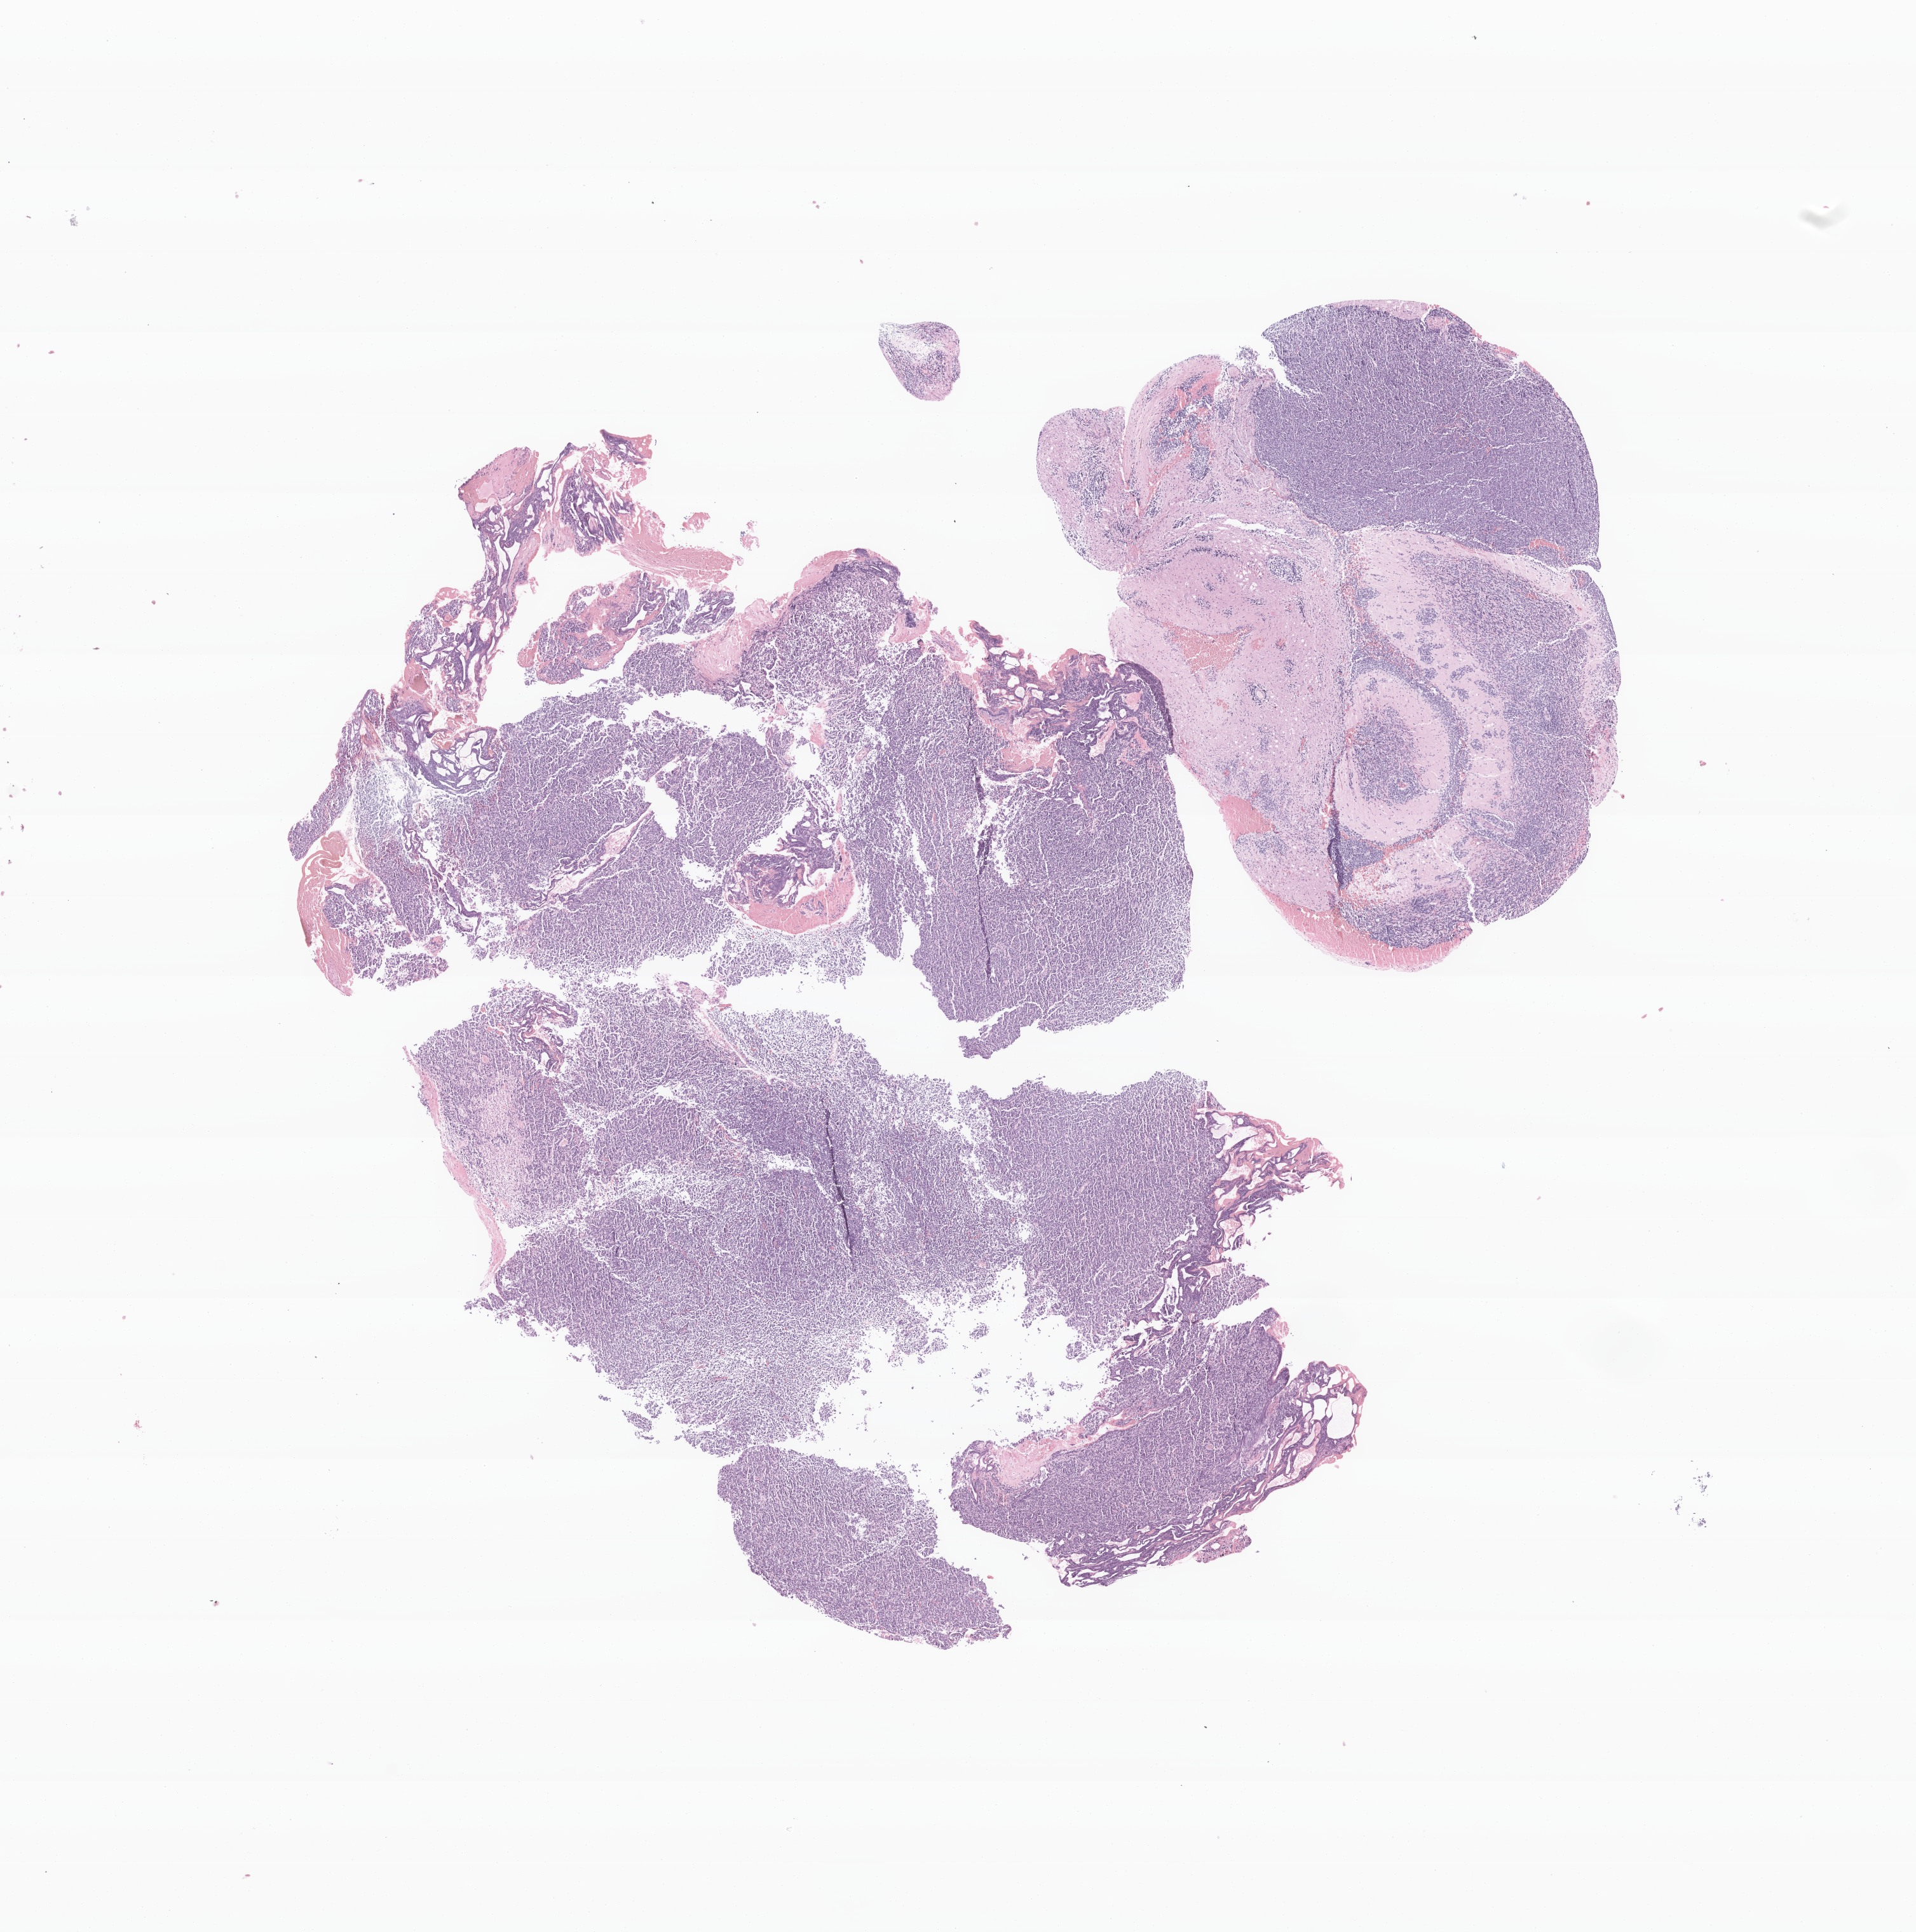
Hematoxylin and eosin (H&E) whole-slide image of tumor tissue from the cerebellum — whole scanned area (about 12.7 x 12.8 mm) shown as a low-resolution overview; formalin-fixed, paraffin-embedded (FFPE) tissue. Patient female; age 200 months (16 years 8 months).
* diagnosis: Medulloblastoma, NOS